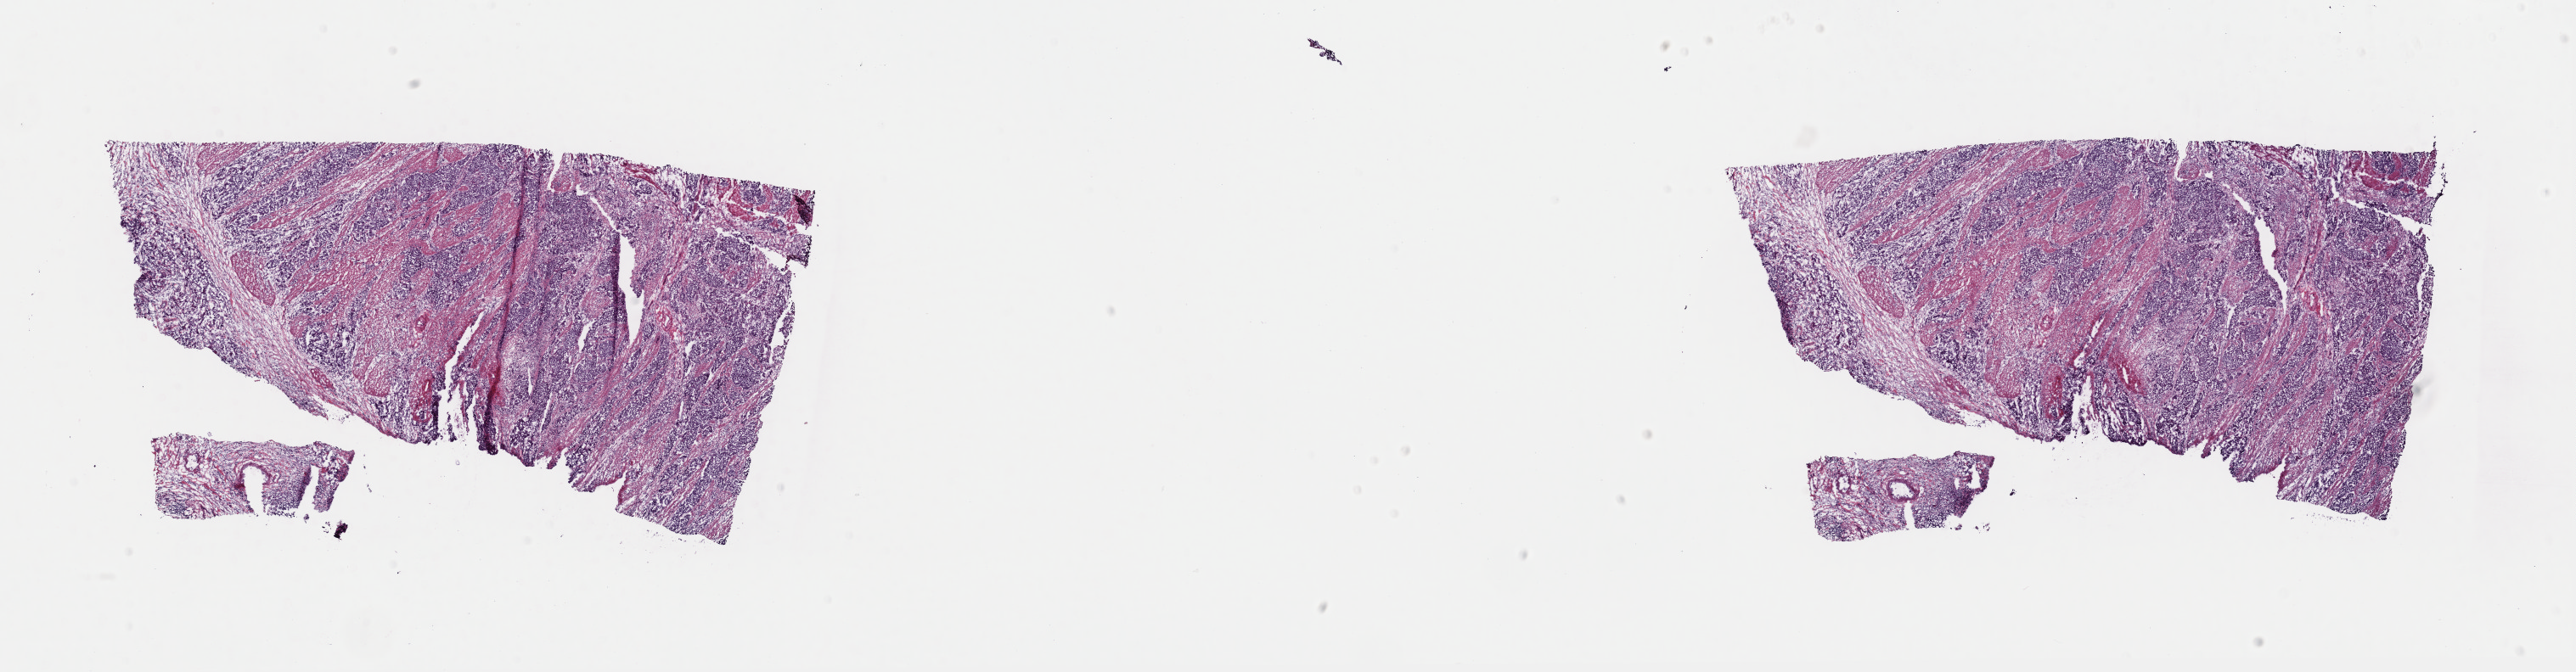
Digitized H&E-stained tissue section (whole slide), shown as a low-resolution overview of the whole scanned area (about 24.0 x 6.3 mm, from a 40x scan). Frozen section from the top of the tissue portion. Sample: primary tumour, esophagus. Male, age 71 years at initial diagnosis.
Pathologic diagnosis: Squamous cell carcinoma, NOS.